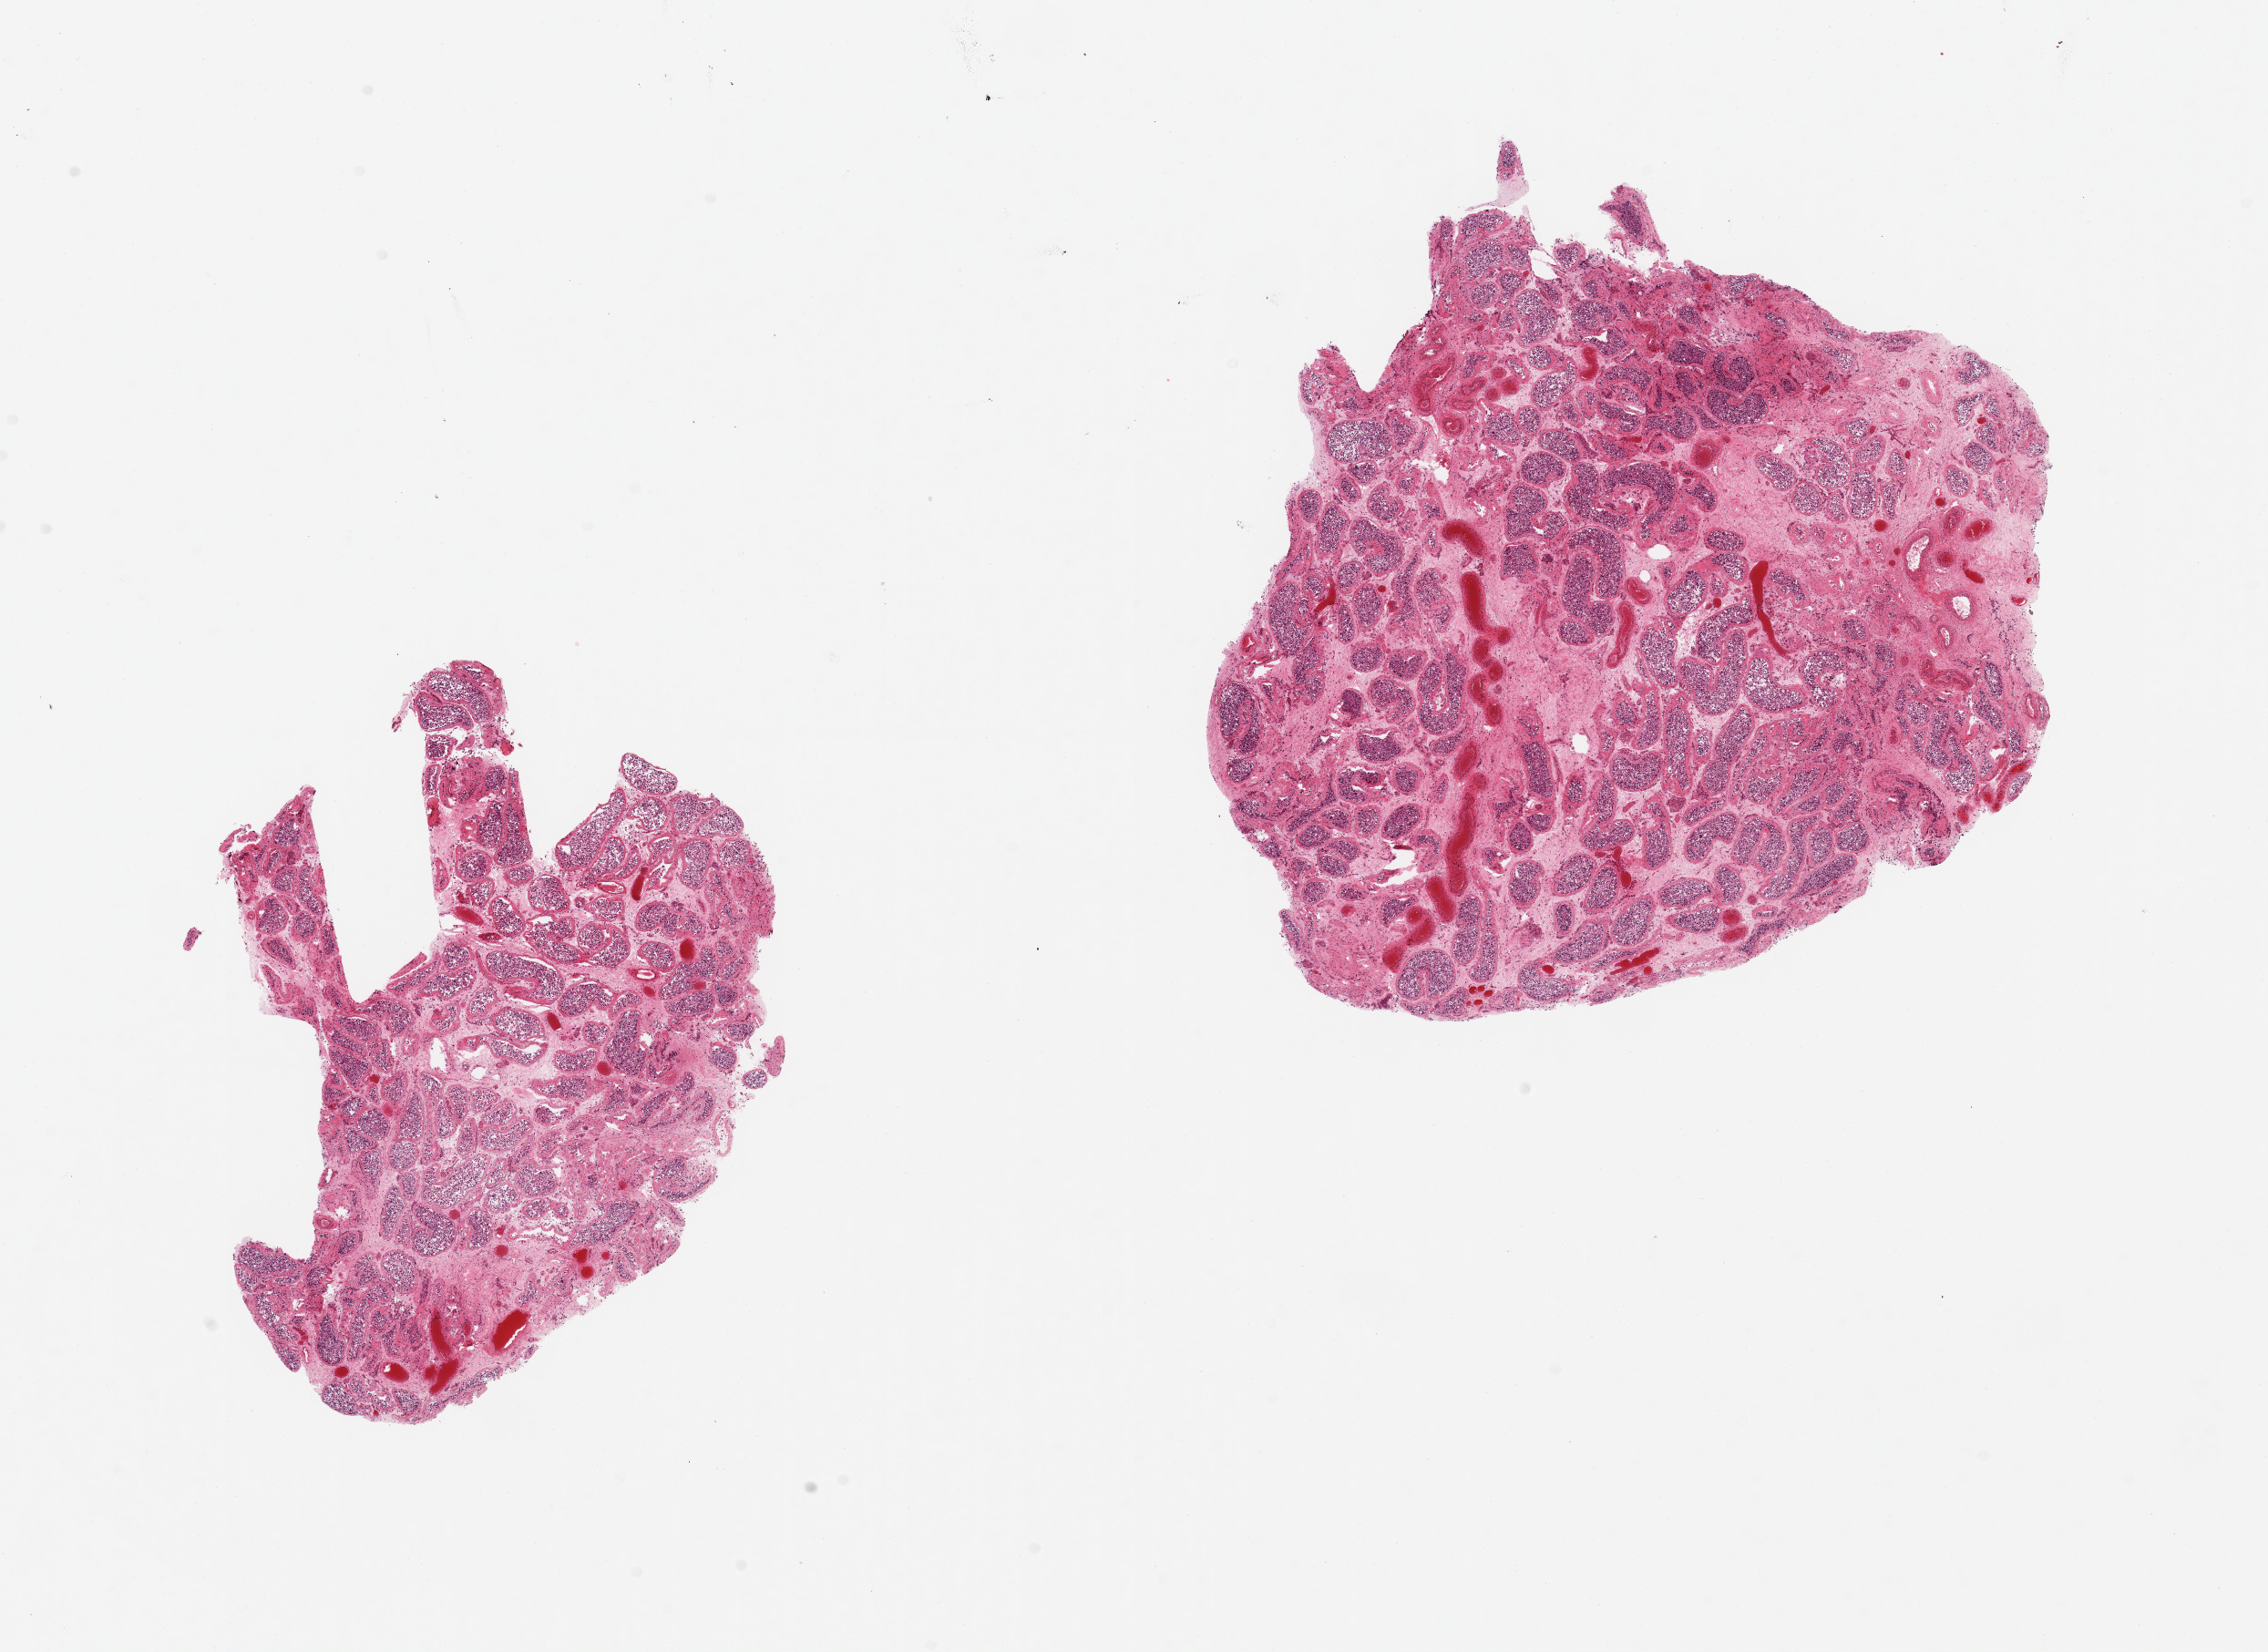
Whole-slide image, haematoxylin and eosin stain, whole scanned area (about 19.7 x 14.3 mm, acquisition: 20x scan) shown as a low-resolution overview; PAXgene-fixed, paraffin-embedded tissue; sampled site (target tissue): testis; tissue donor sample. Donor sex: male.
• reviewer comment on this tissue sample: 2 aliquots, ~7x5mm. Patchy infarcts/scars, badly autolyzed